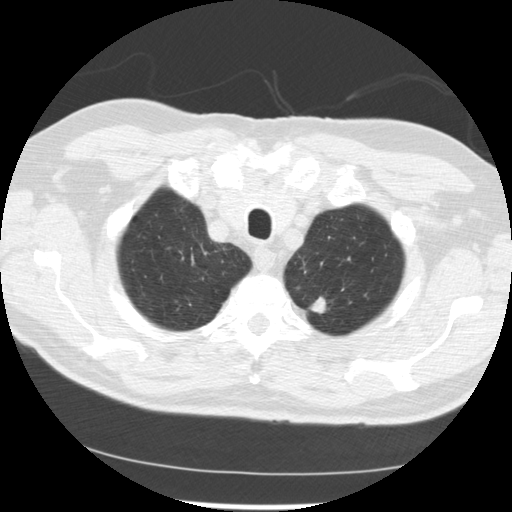
Low-dose screening chest CT, one axial slice. Slice 217 of 249 in the series (ordered by position). 120 kVp. Lung window (W 1500 / L -600 HU). 2.5 mm slice thickness. 512 × 512 image matrix, field of view 341 × 341 mm.
Outlined on this slice (expert manual segmentation):
- lesion 2 (tumor, upper lobe of left lung): bounding box [x1, y1, x2, y2] px = [311, 297, 326, 314]